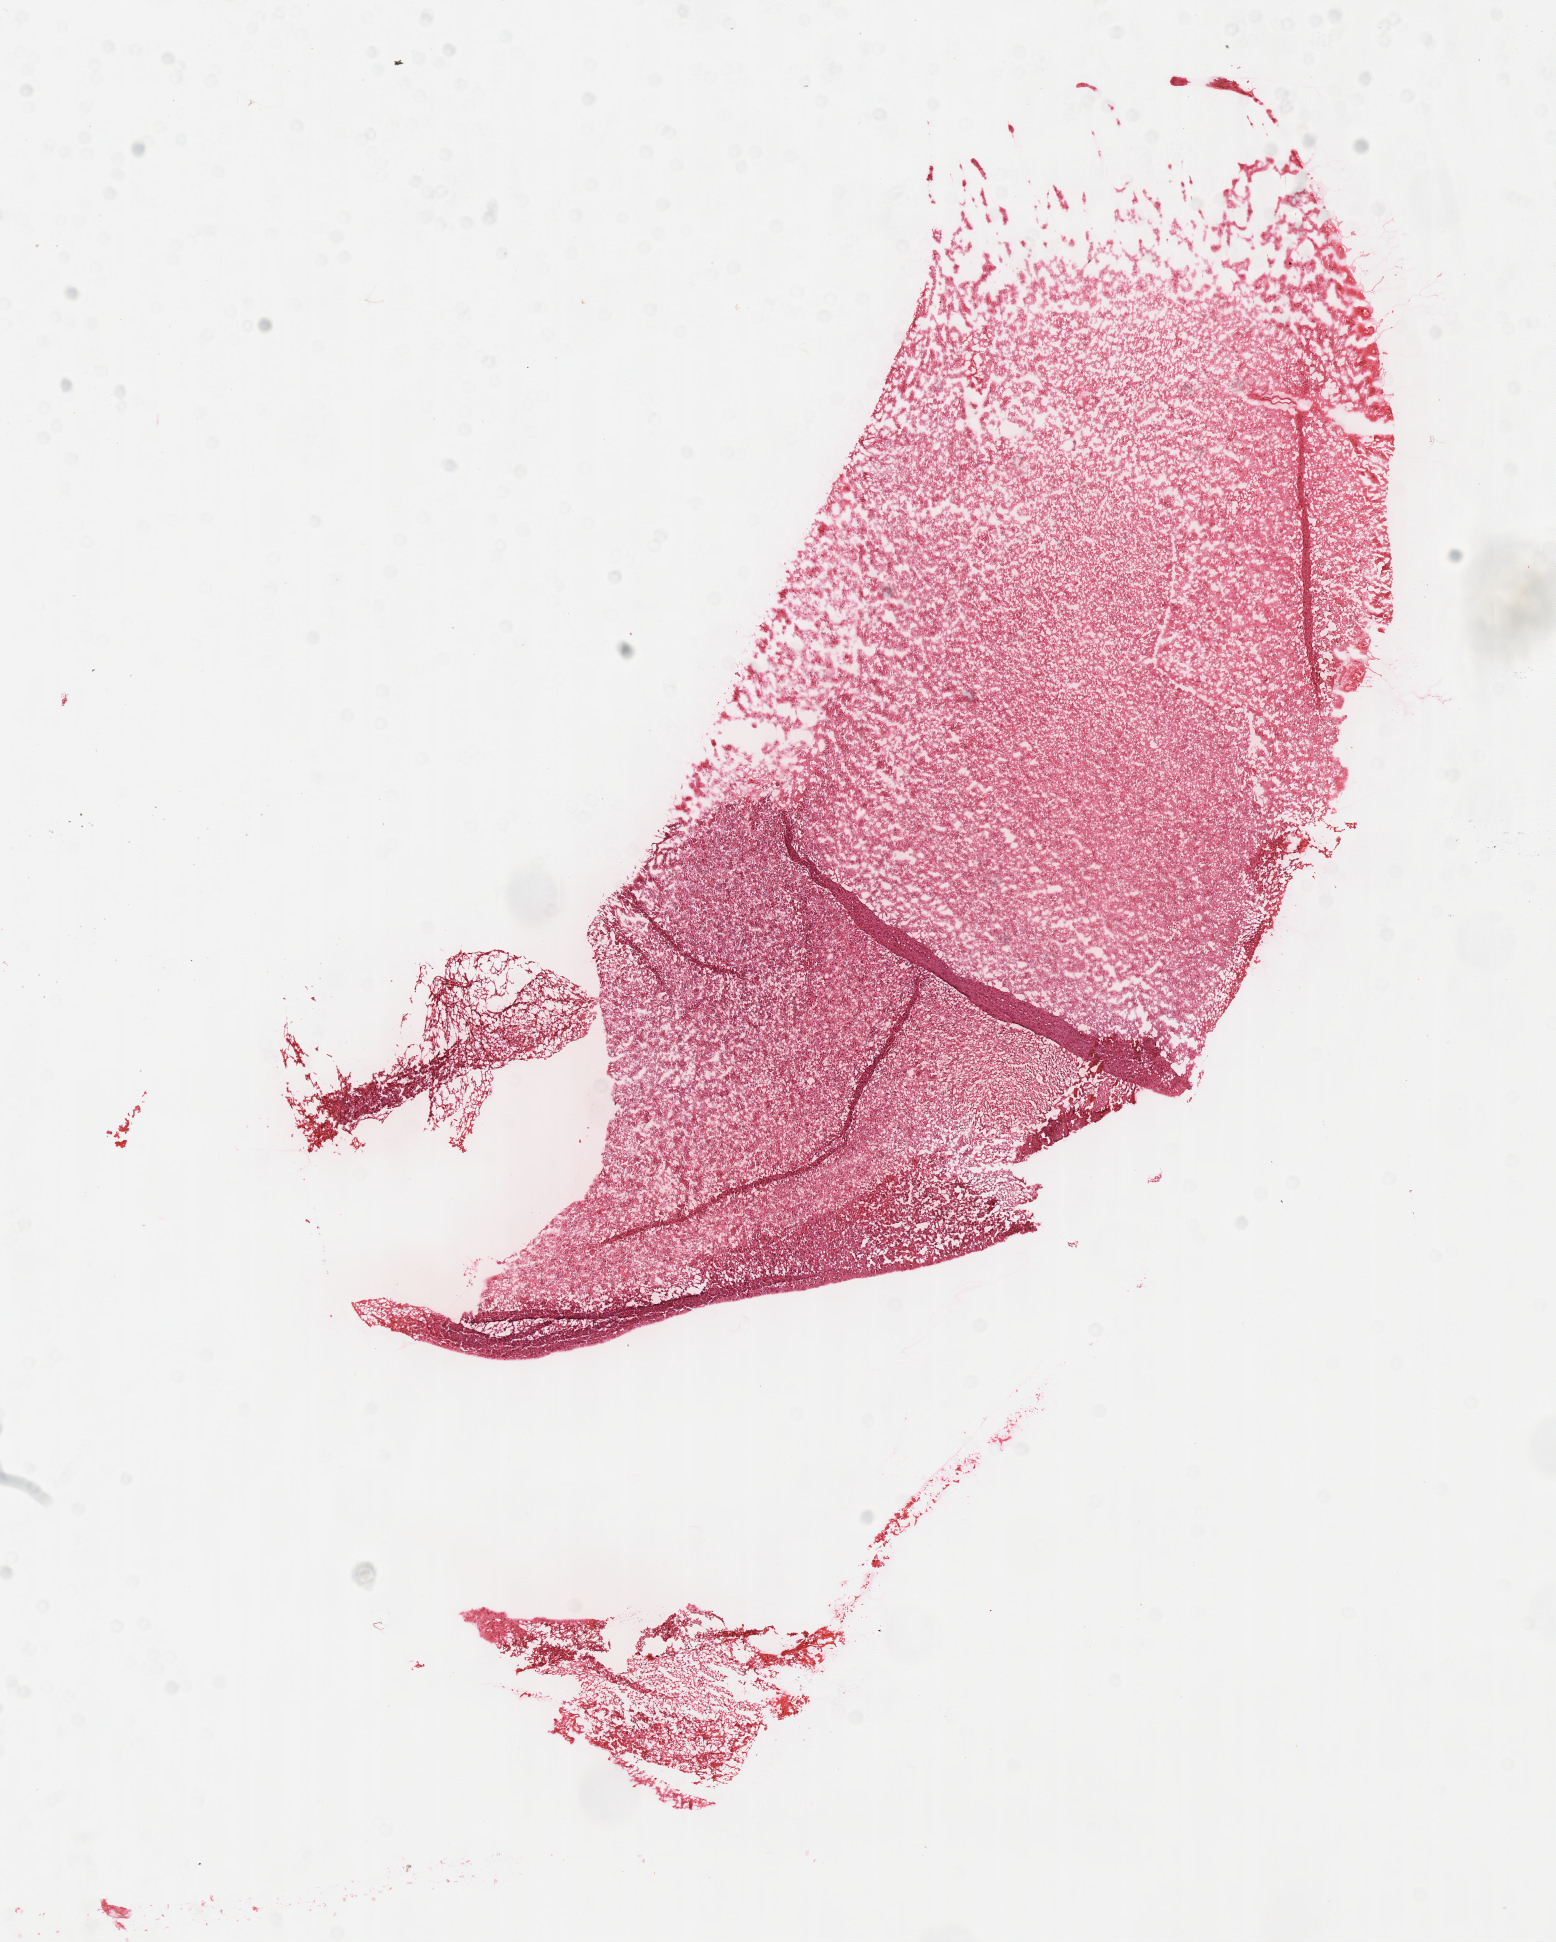
Whole-slide histology image, H&E, a low-resolution overview of the entire scanned area, about 12.6 x 15.7 mm (from a 40x scan), frozen section from the top of the tissue portion, sample: primary tumour, brain. Patient: female, age at initial diagnosis 49 years. Pathologist review of this section (percent, as recorded): tumour cells 85%, tumour nuclei 95%.
Pathologic diagnosis: Glioblastoma.